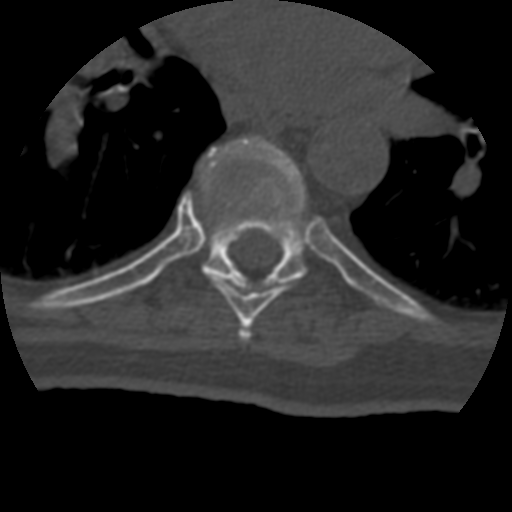
CT including the spine, one axial slice. Slice 271 of 399 in the series (ordered by position). 120 kVp. Bone window (W 1800 / L 400 HU). 1.25 mm slice thickness. 512 × 512 image matrix, field of view 160 × 160 mm. Patient age 69 years. From the clinical record (not read from this slice): primary cancer: prostate.
Annotated regions visible in this slice (semi-automatic segmentation, software-assisted and operator-edited):
- T6 vertebra: box from (x=239, y=329) to (x=249, y=340) px
- T7 vertebra: (x=200, y=165)–(x=288, y=328)
- T8 vertebra: (x=163, y=135)–(x=309, y=300)